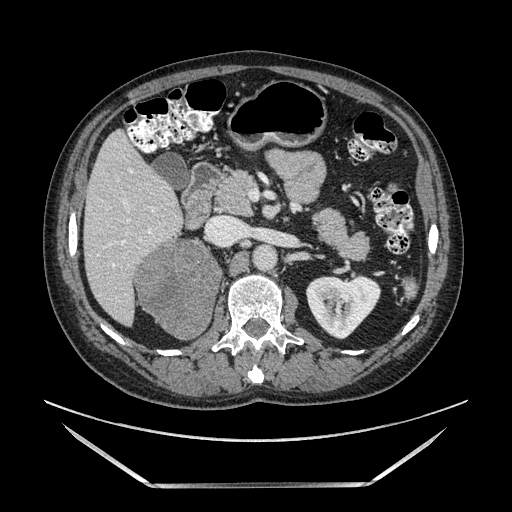
Contrast-enhanced abdominal CT, one axial slice. Soft-tissue window (W 400 / L 40 HU). 1.25 mm slice thickness. 512 × 512 image matrix, field of view 440 × 440 mm. Male patient. Case-level facts recorded for this patient, not image findings: diagnosis: adrenocortical carcinoma; tumour side: right adrenal; tumour size at pathology: 10.3 cm; Ki-67 index: 20 %.
Outlined on this slice (semi-automatically segmented with operator editing):
- mass: bounding box (x1, y1, x2, y2) in pixels: (137, 240, 217, 337)